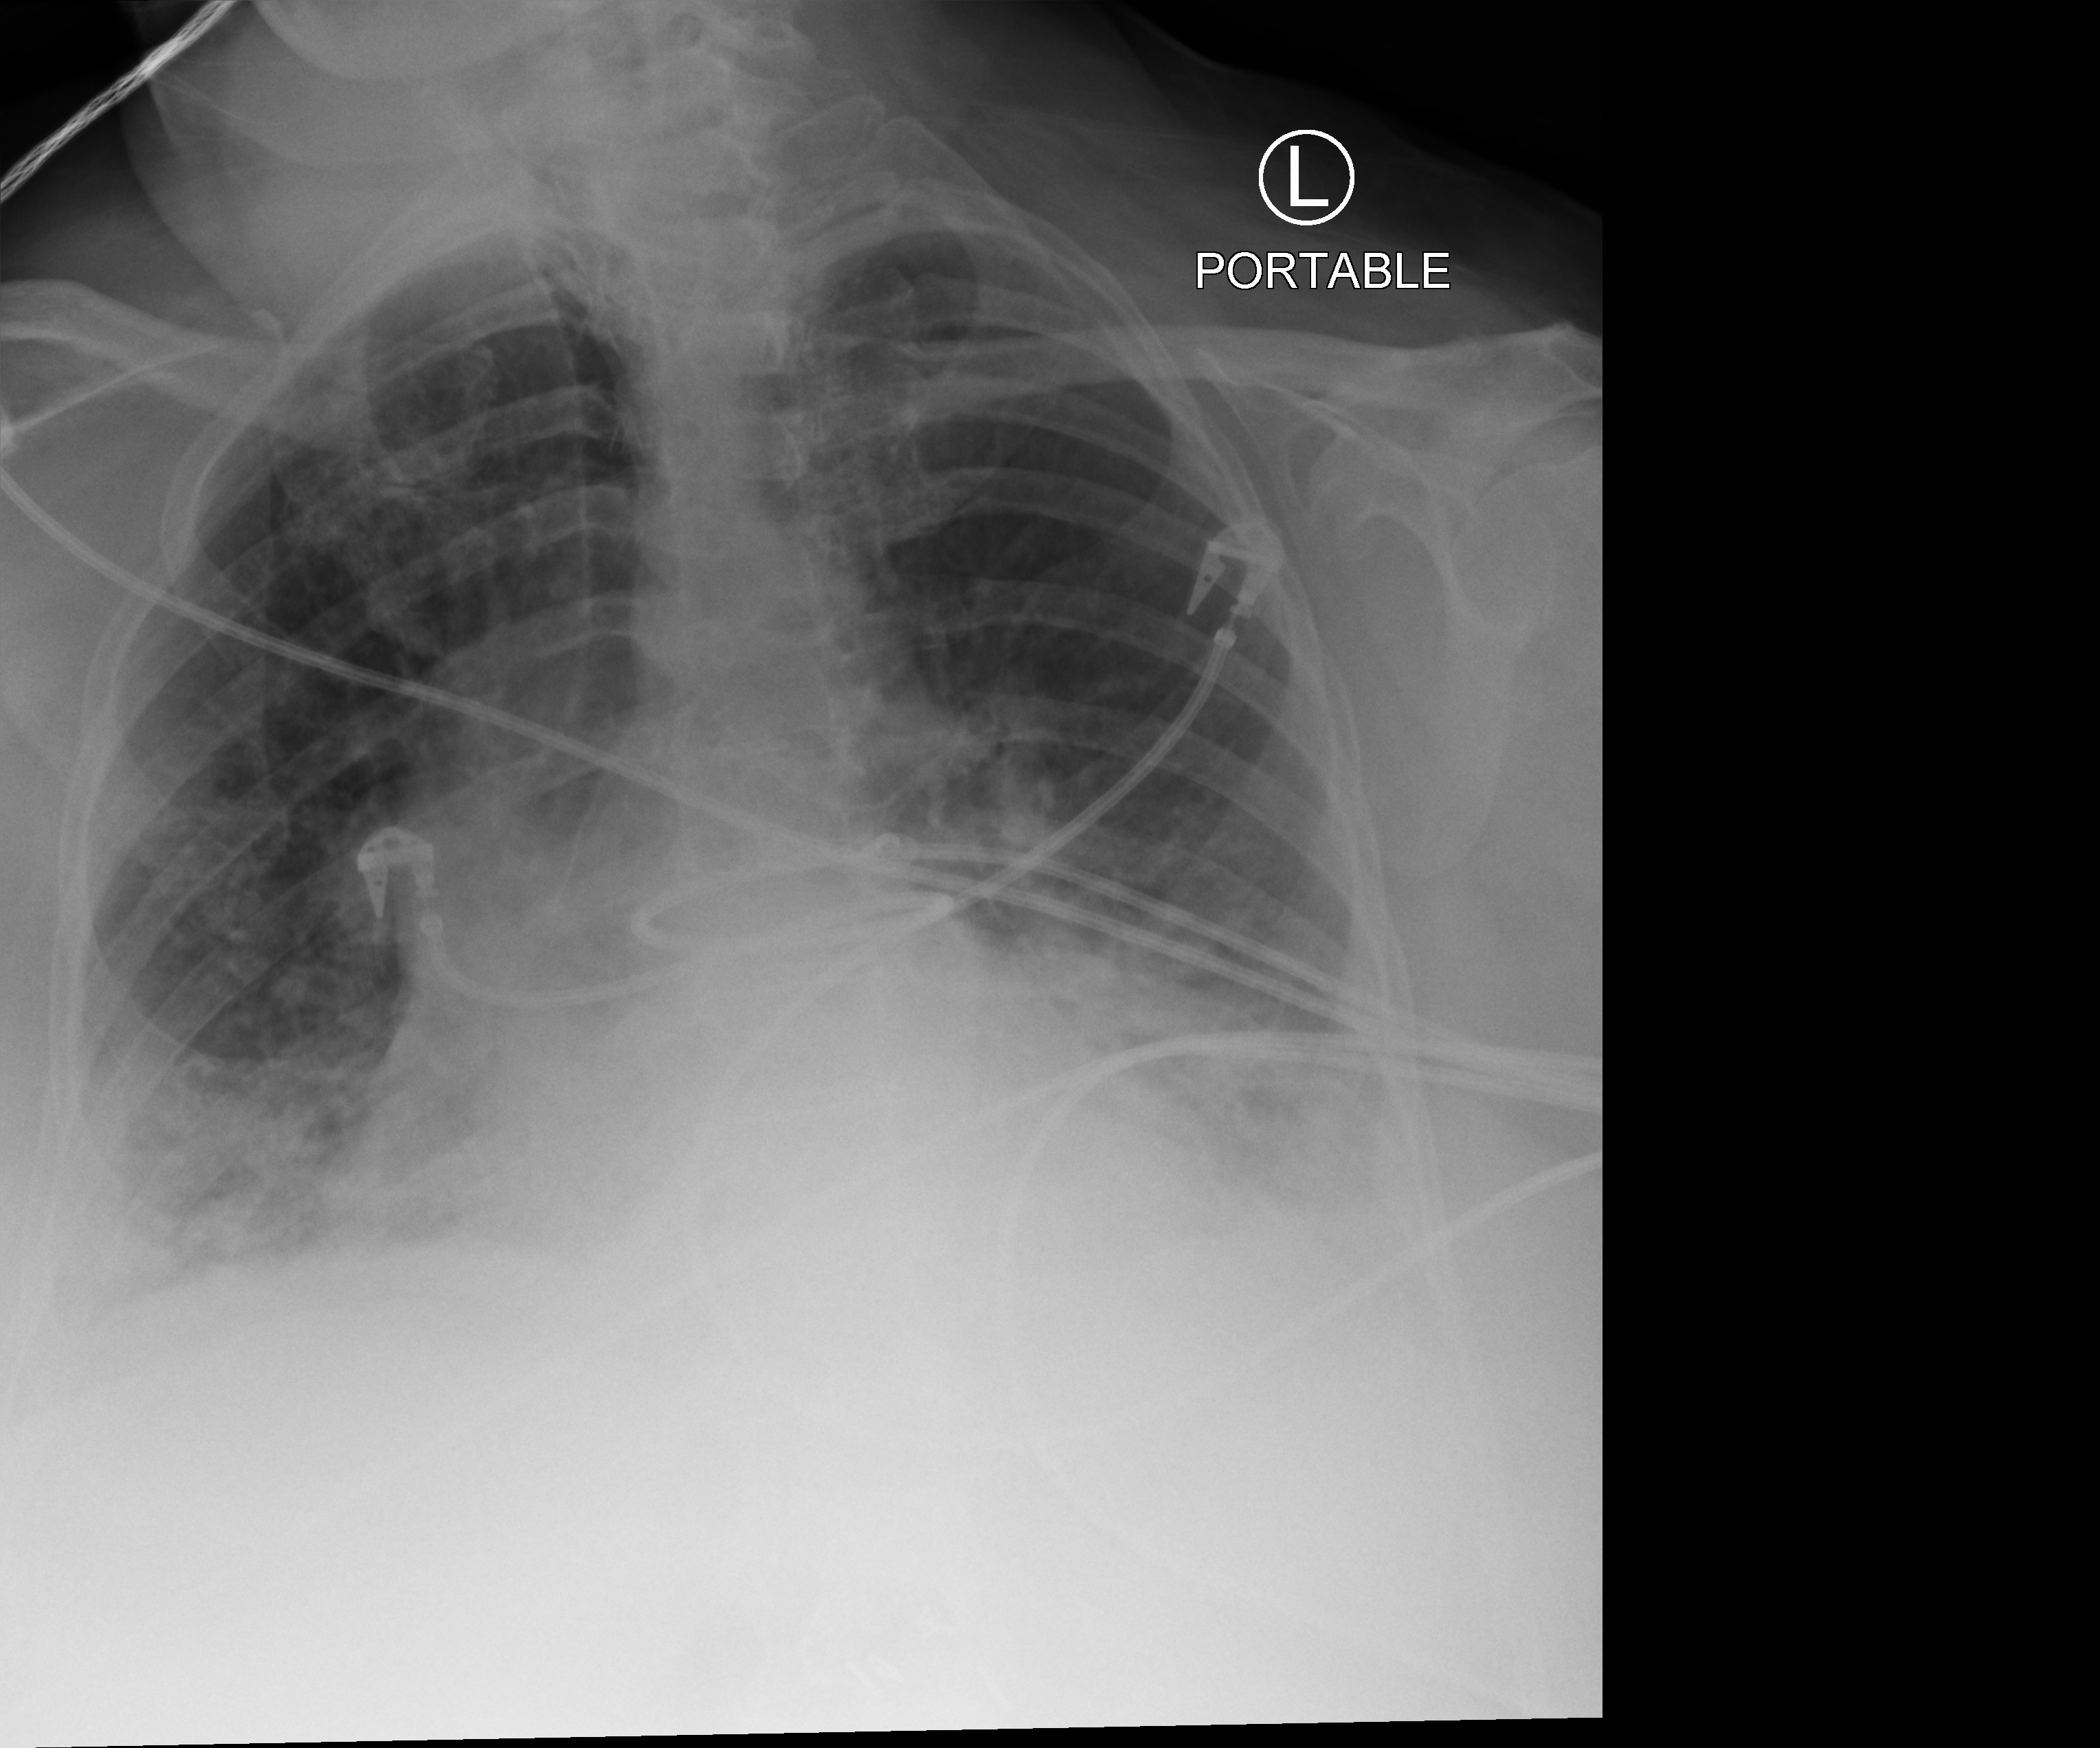
Chest X-ray (portable). Female patient hospitalised with COVID-19, age 75–90 years.
From the hospital-stay record, not from the radiograph (when in the stay this image was taken is not recorded): mechanically ventilated during this hospital stay: no; hypertension (admission record): yes.